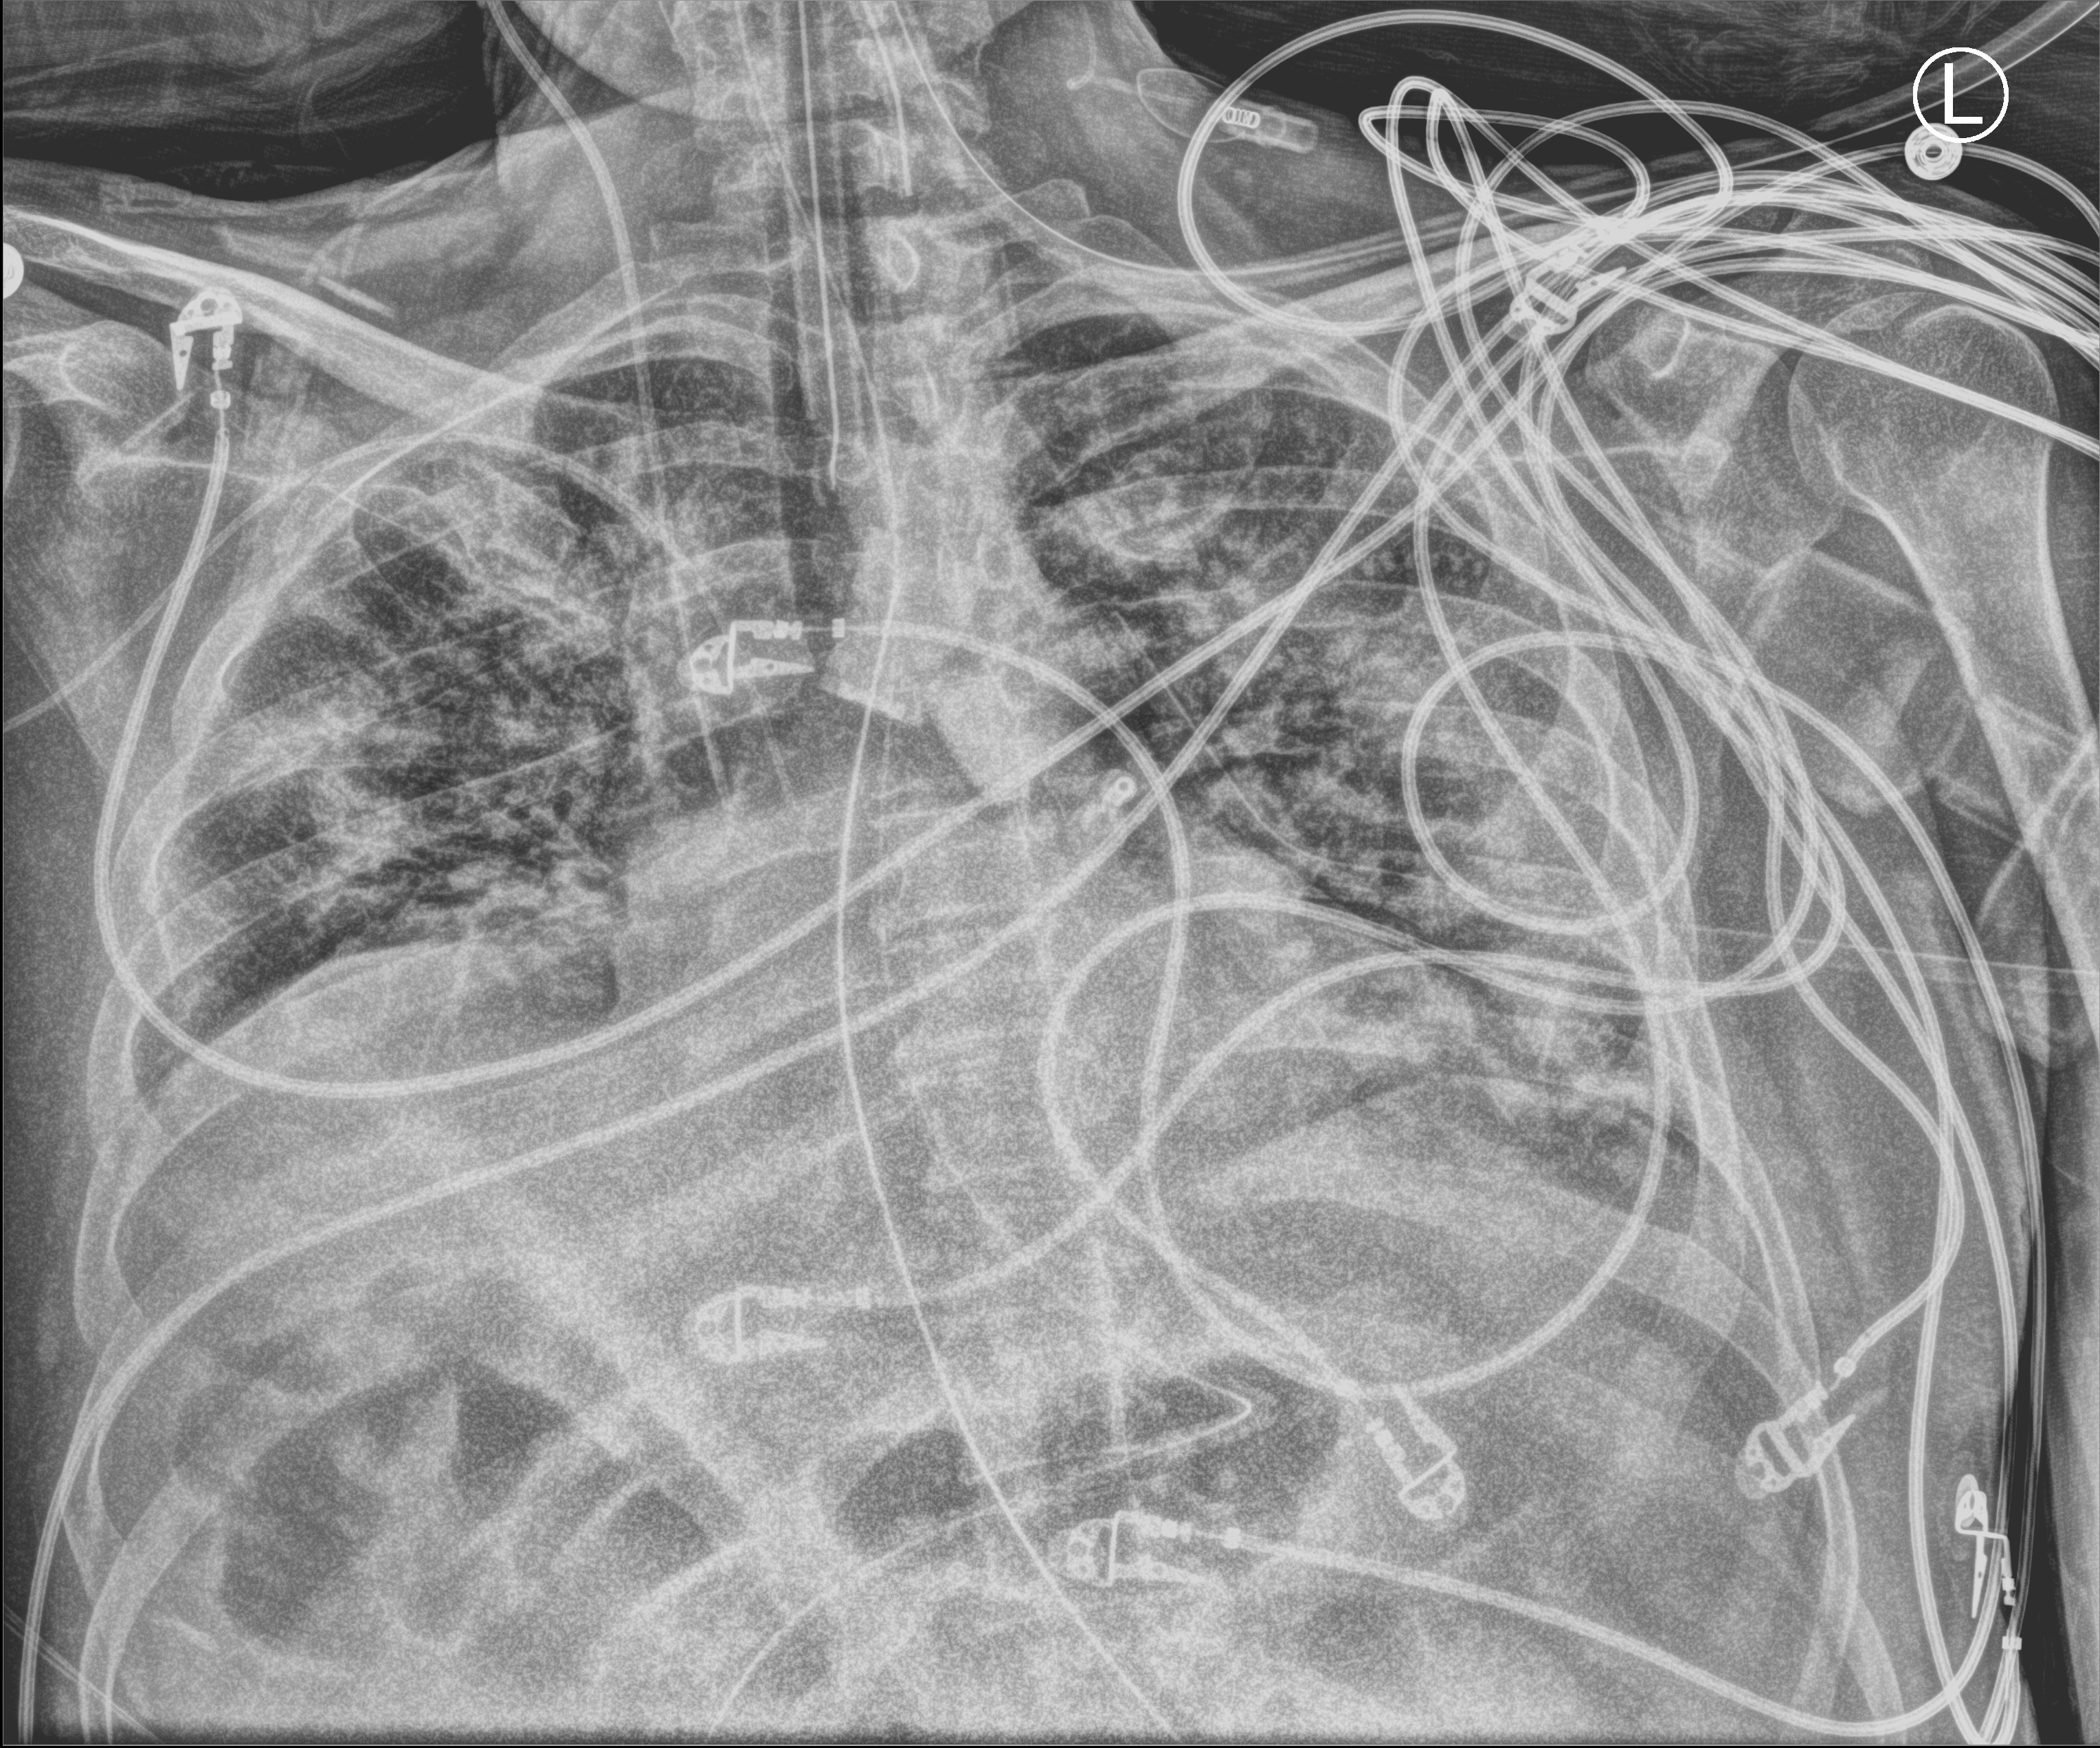
Chest X-ray (portable), anteroposterior (AP) projection. Patient hospitalised with COVID-19; male, aged 18–59 years.
Hospital-stay facts (about this admission, not read from this image; timing relative to this image not recorded):
- admitted to intensive care during this hospital stay: yes
- mechanically ventilated during this hospital stay: yes